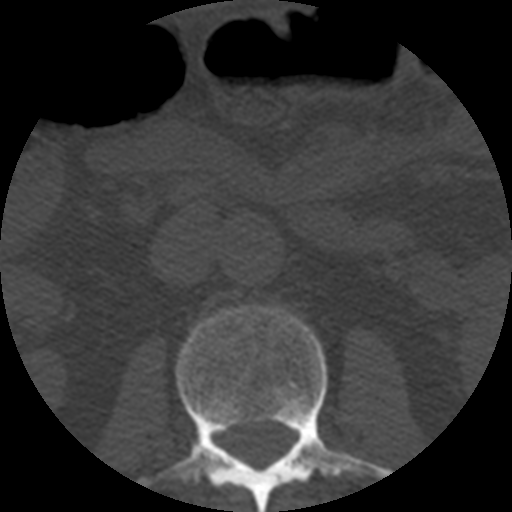
CT including the spine, one axial slice; position 151 of 508 along the scan axis; reconstruction kernel STANDARD; bone window (W 1800 / L 400 HU); 1.25 mm slice thickness; 512 × 512 image matrix. Patient age 57 years. Case-level facts recorded for this patient, not image findings: primary cancer: prostate.
Annotated regions visible in this slice (semi-automatic segmentation, software-assisted and operator-edited):
- L2 vertebra: bounding box [x1, y1, x2, y2] px = [141, 306, 391, 512]